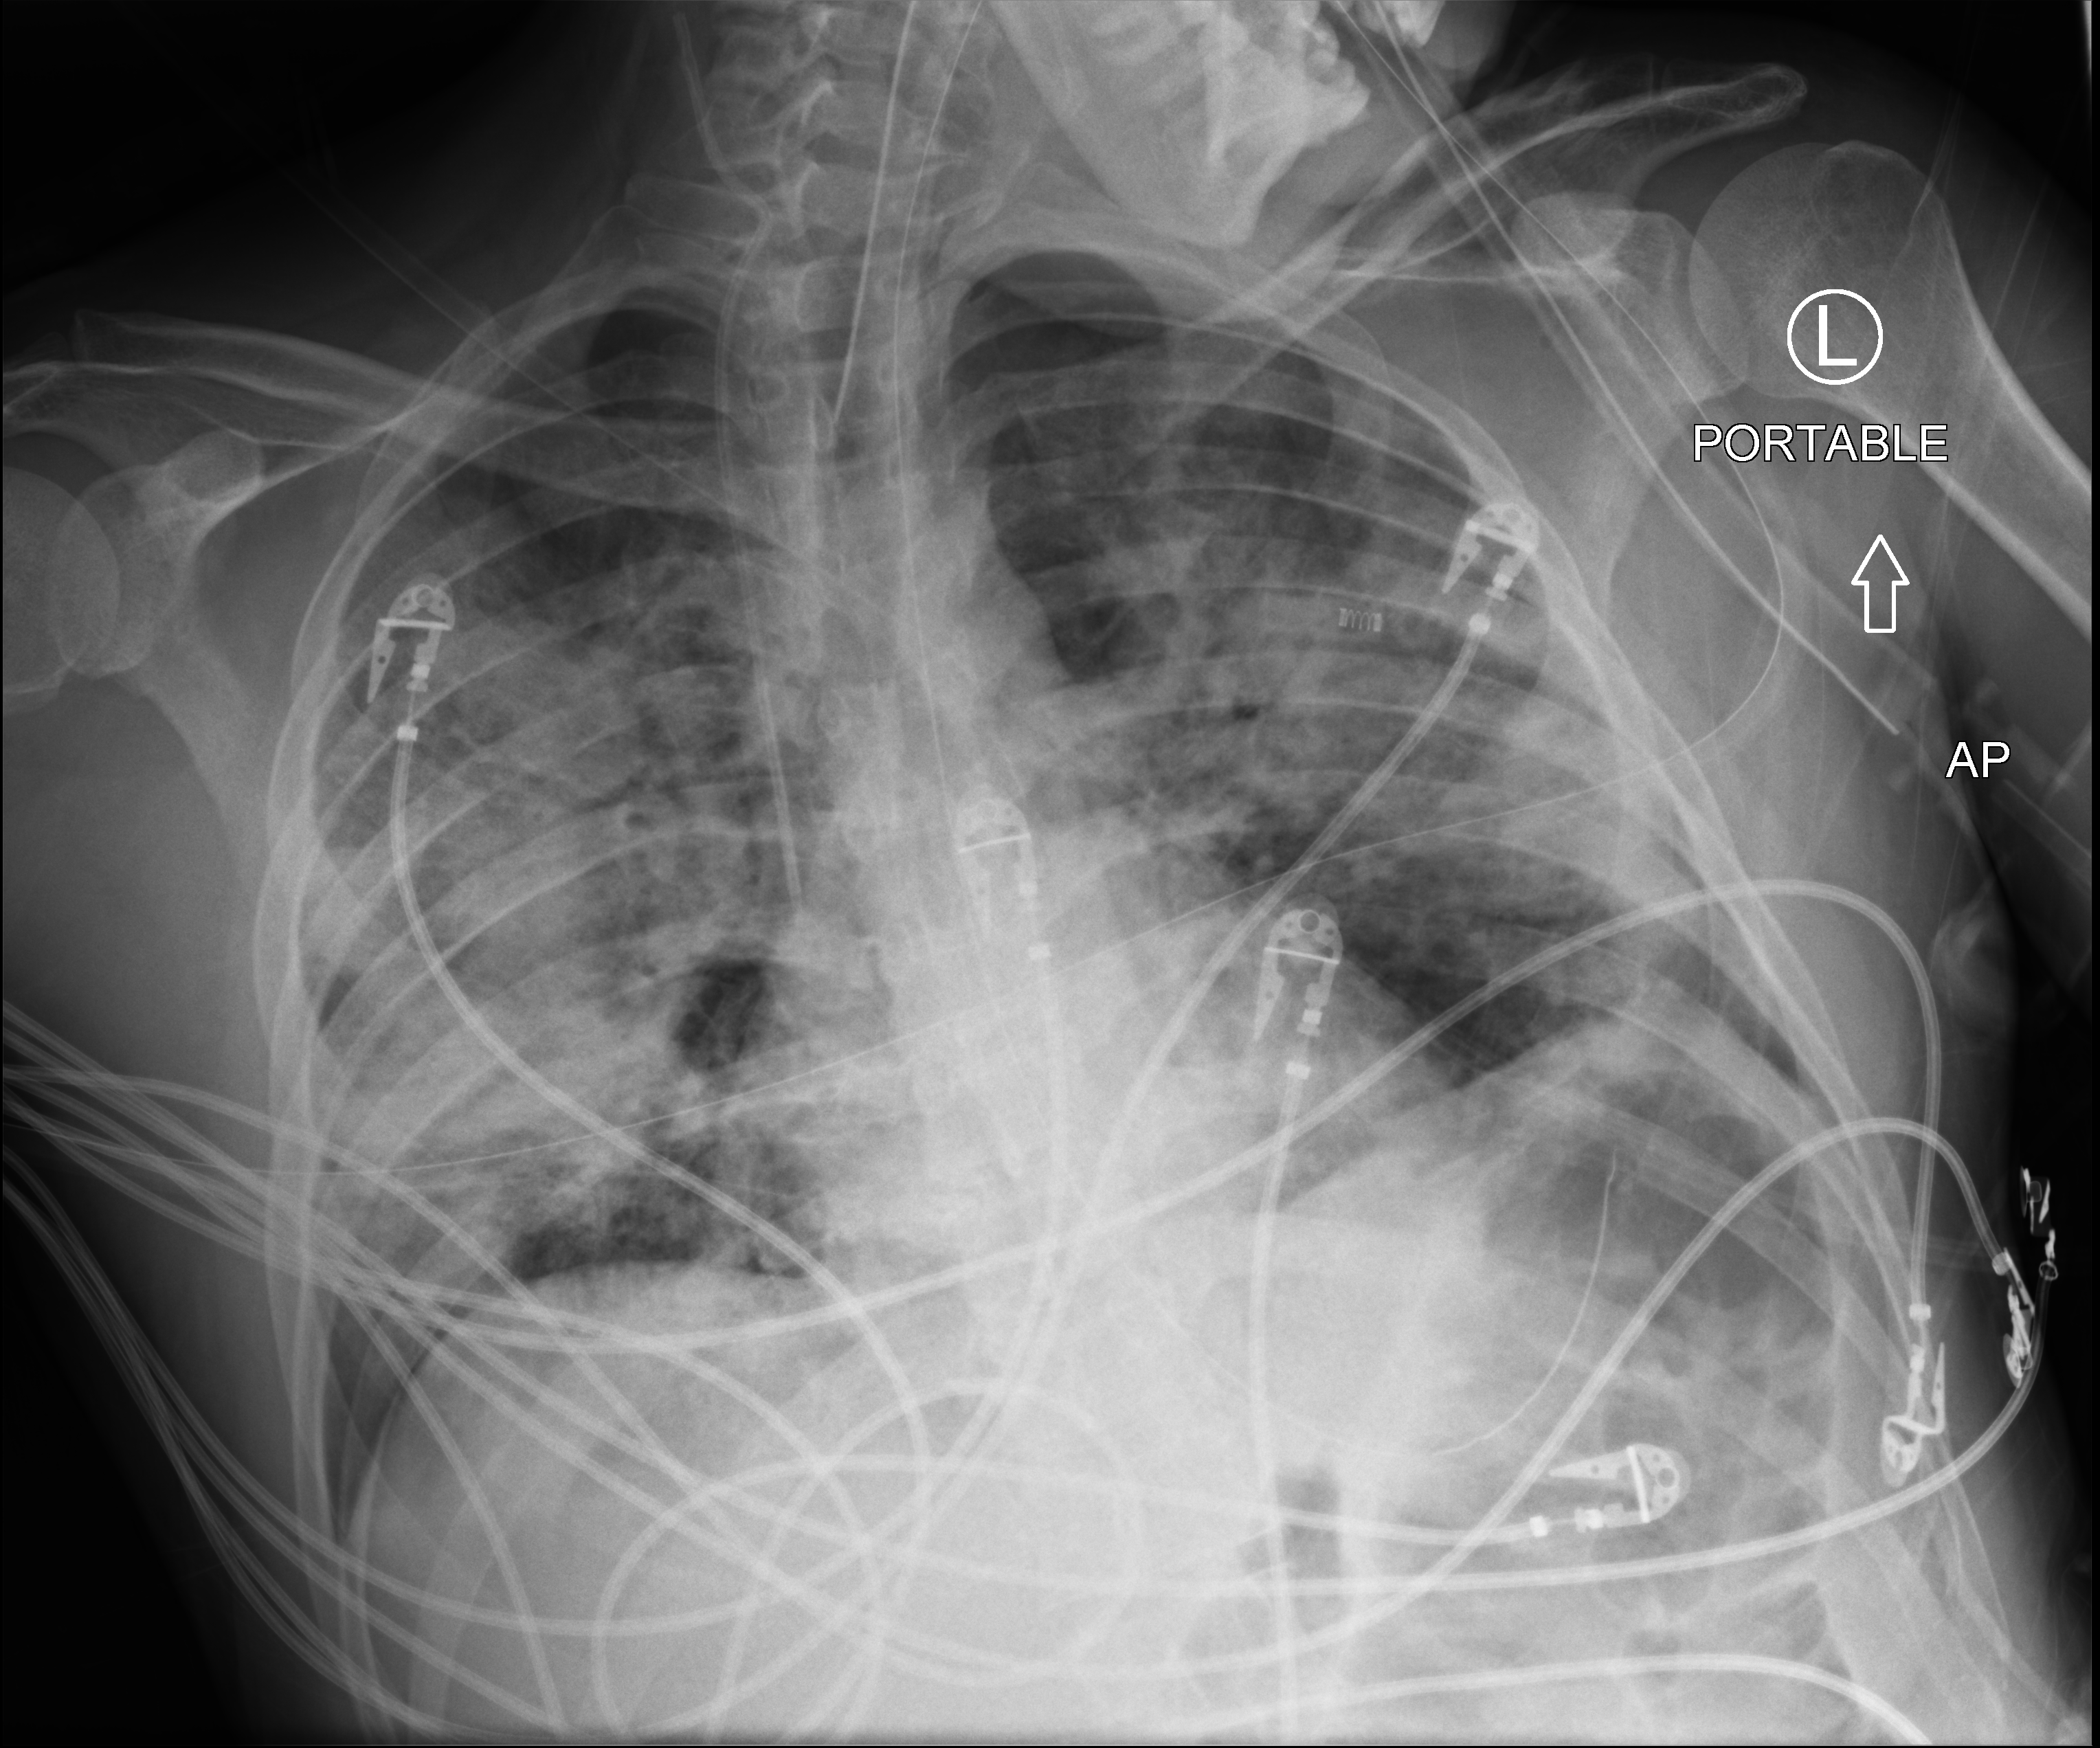
Portable chest radiograph, anteroposterior (AP) projection. Patient hospitalised with COVID-19; male, aged 18–59 years.
Hospital-stay facts (about this admission, not read from this image; timing relative to this image not recorded): admitted to intensive care during this hospital stay: yes; mechanically ventilated during this hospital stay: yes; chronic kidney disease (admission record): no.